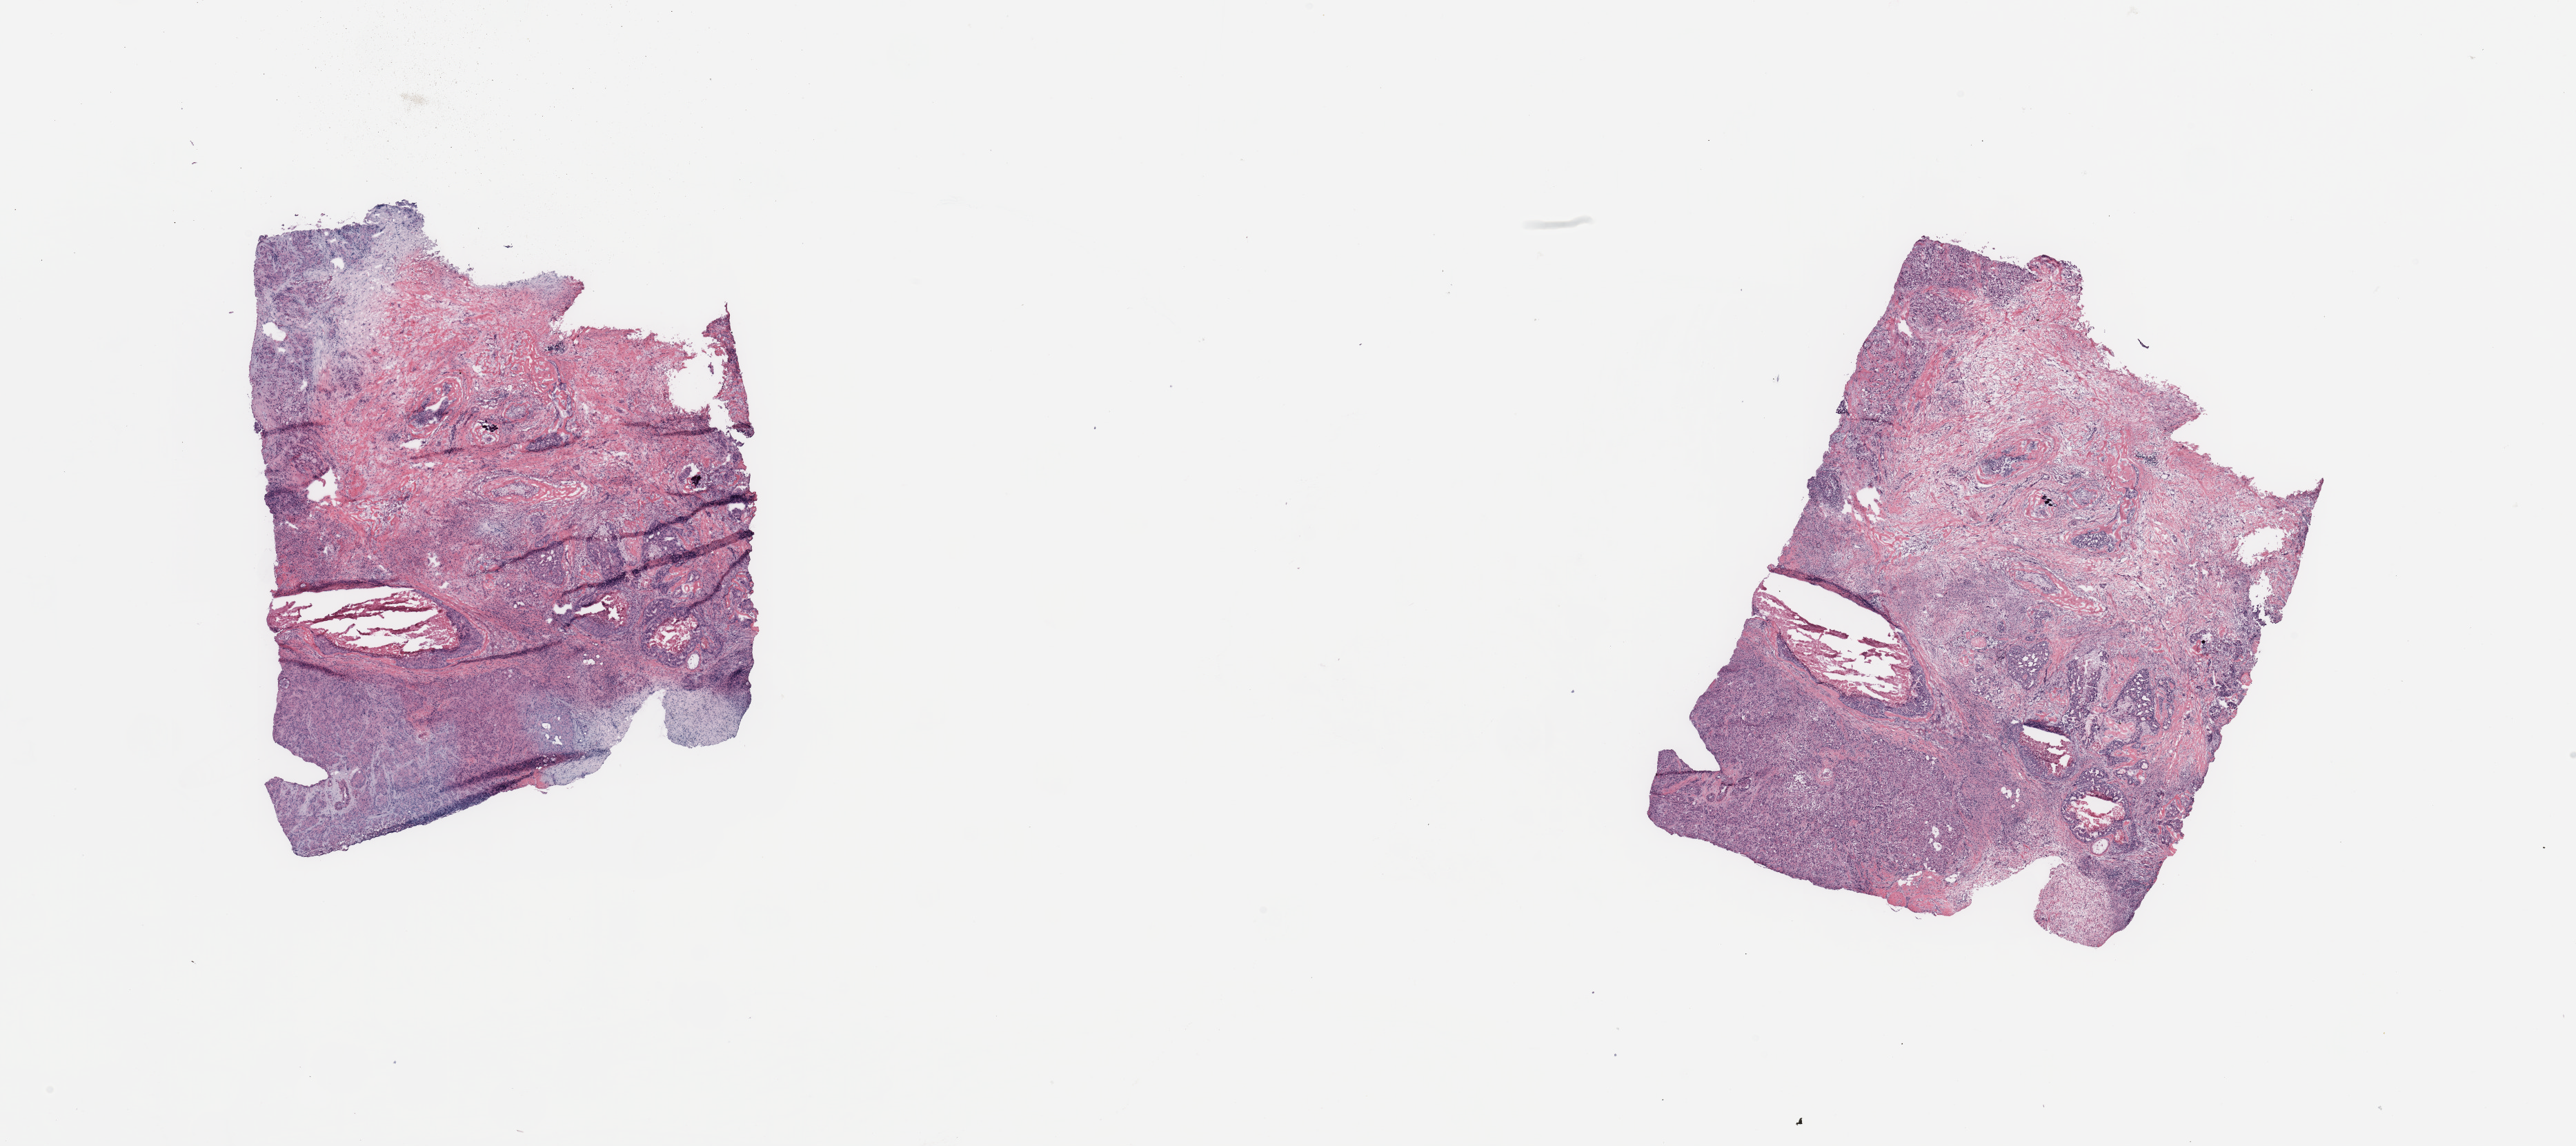
Whole-slide histology image, H&E-stained, low-resolution overview of the scanned area, about 29.5 x 13.1 mm (slide scanned at 20x); breast, tumour tissue. Patient: female, age 62 years.
Histologic diagnosis: Infiltrating duct carcinoma, NOS. AJCC pathologic stage: IIB.